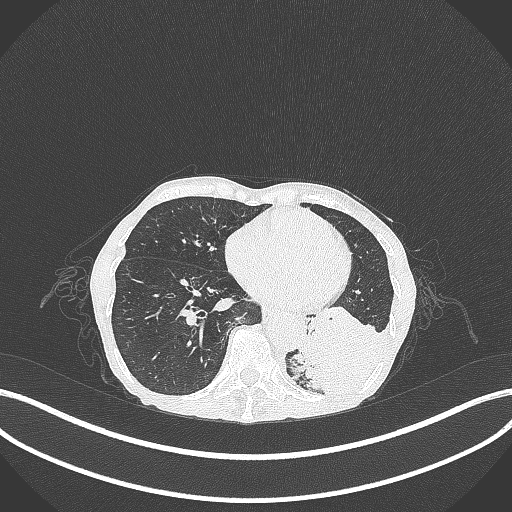
Chest CT, one axial slice. Position 87 of 347 along the scan axis. 120 kVp. Lung window (W 1500 / L -600 HU). 1 mm slice thickness. 512 × 512 image matrix, field of view 400 × 400 mm. Female patient, age 70 years. From the clinical record (not read from this slice): clinical TNM (as recorded): T3 N0 M0; histopathological grade: G3.
Structures marked on this image (bounding box drawn by a radiologist):
- lung tumour (recorded histology: small cell carcinoma): bounding box <293,310,389,403> (left, top, right, bottom; pixels)